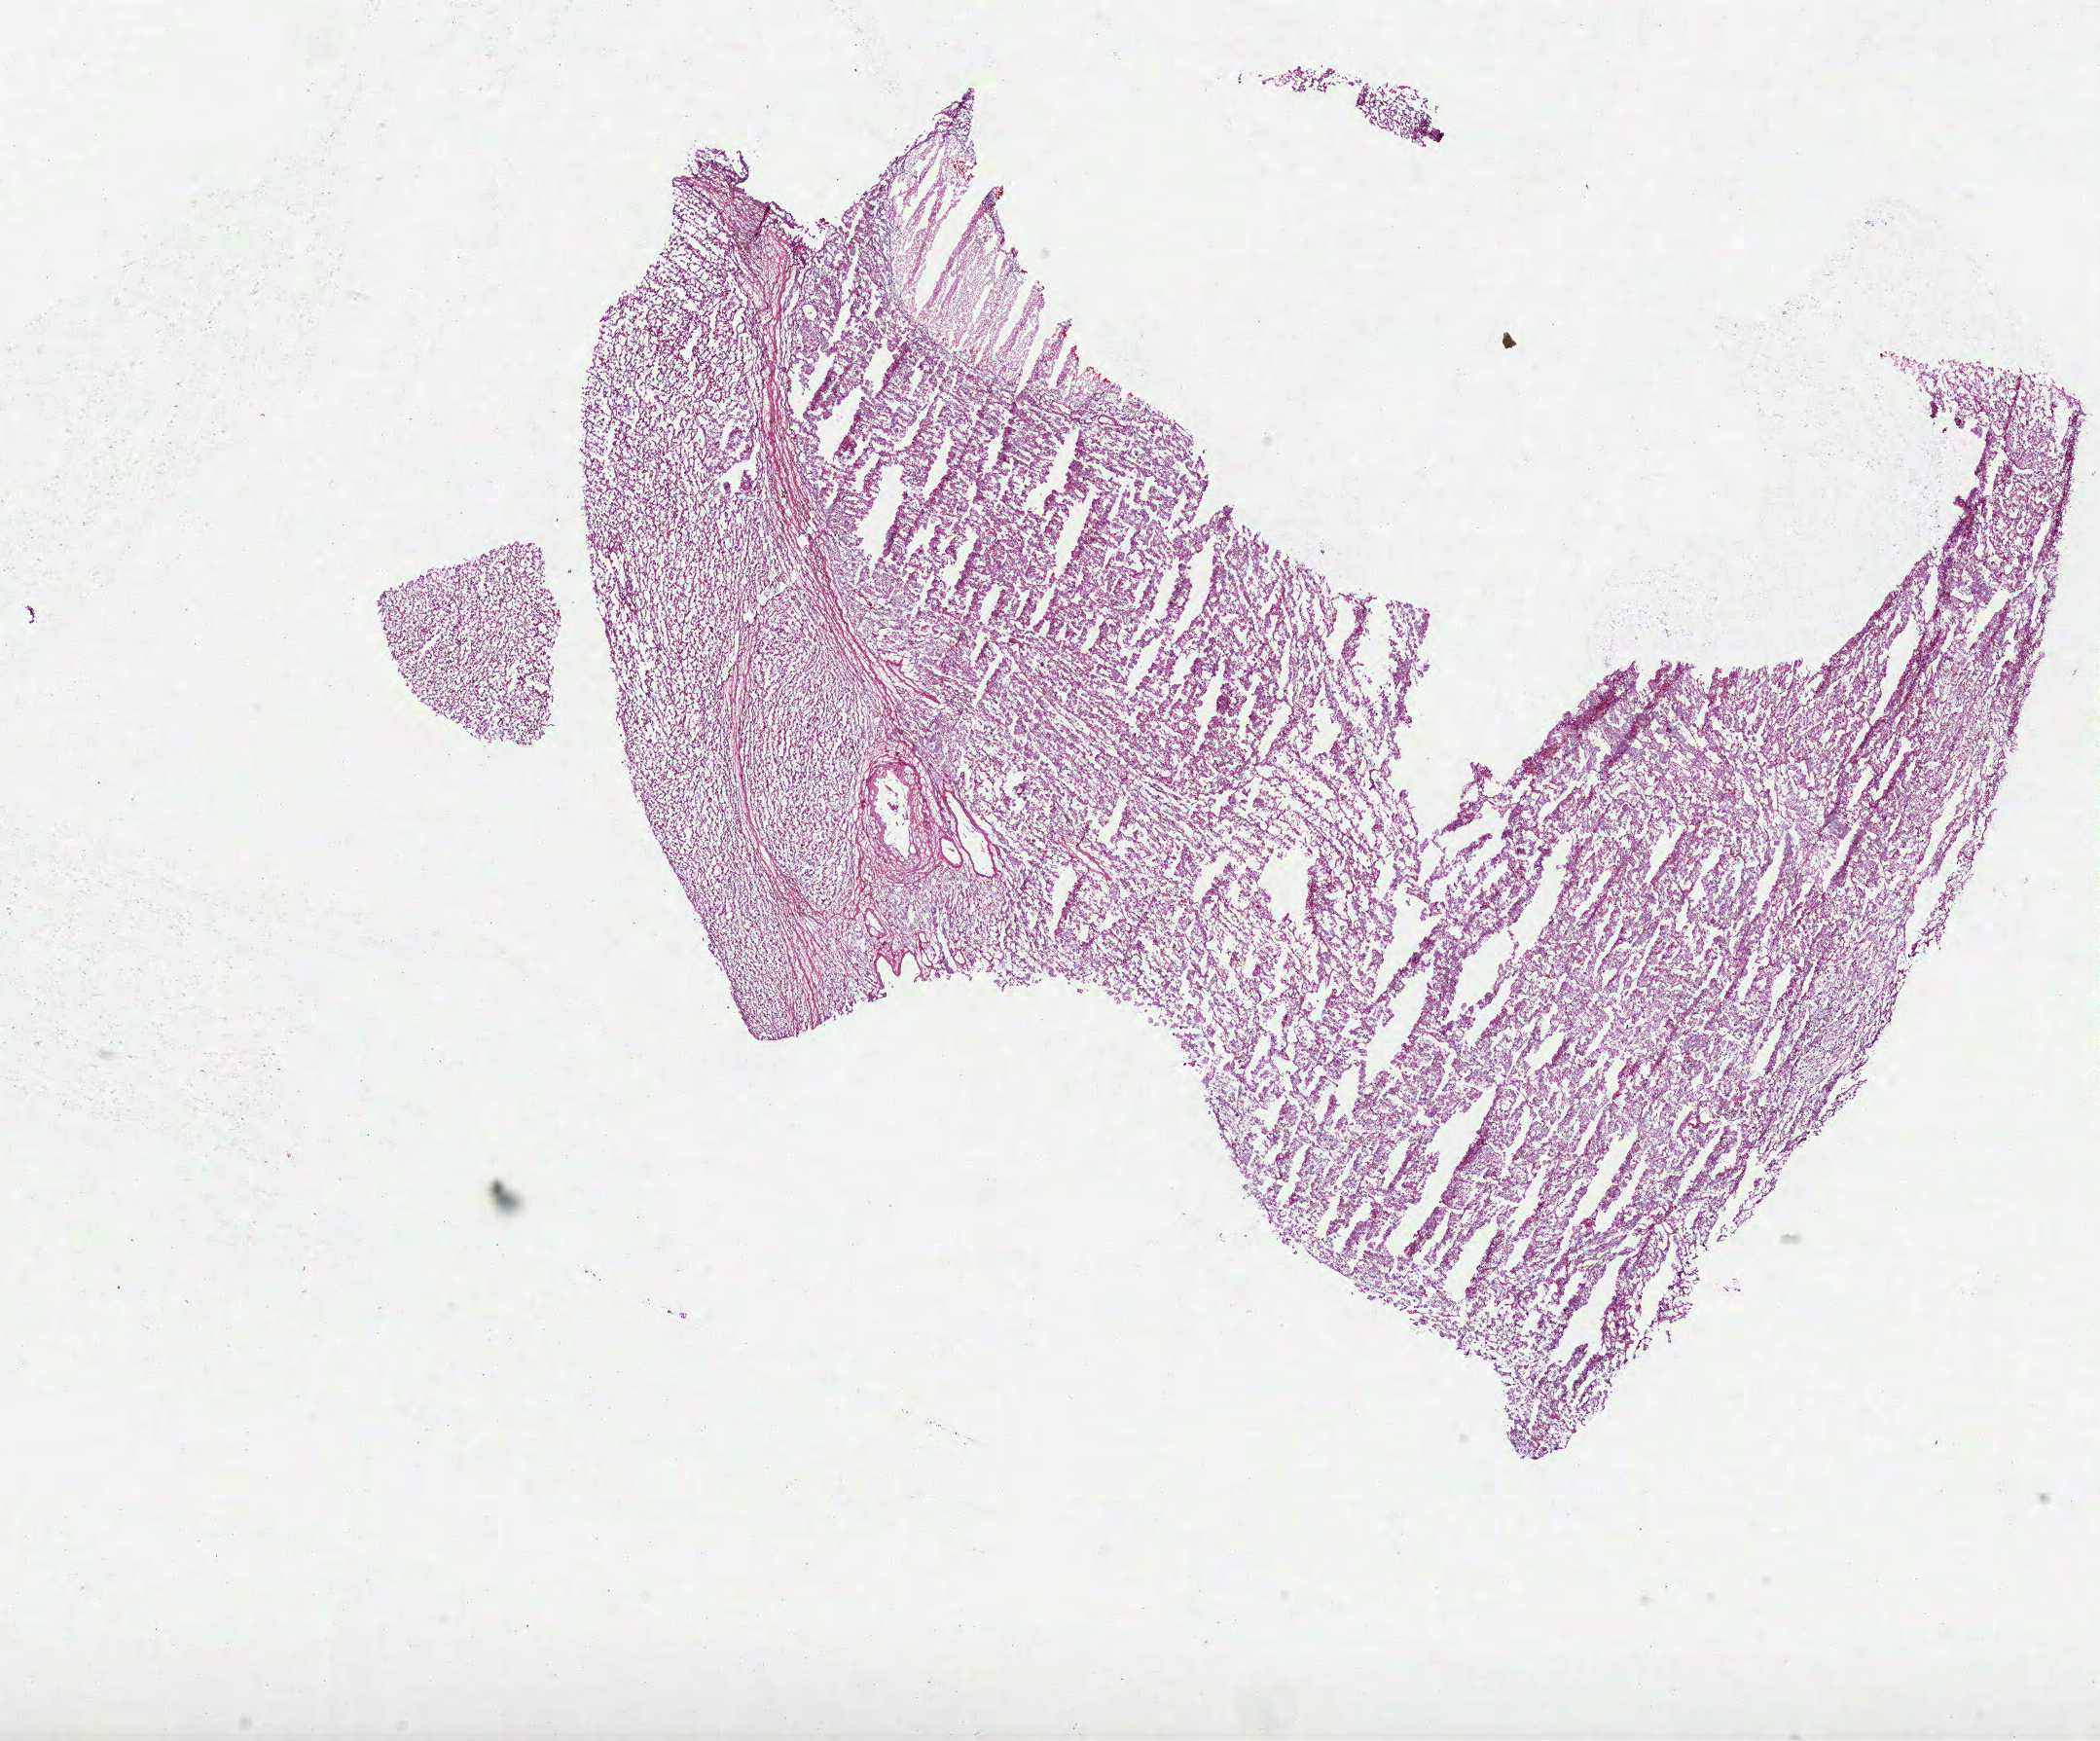
Hematoxylin and eosin (H&E) stained whole-slide image — whole scanned area (about 17.4 x 14.4 mm) shown as a low-resolution overview. Frozen section from the bottom of the tissue portion. Primary tumour sample from the kidney. Patient: female, age at initial diagnosis 46 years. Slide review estimates, as recorded: tumour cells 100%, tumour nuclei 90%, normal cells 0%, stromal cells 0%, necrosis 0%. Inflammatory infiltration, as recorded: lymphocyte infiltration 0%, monocyte infiltration 0%, neutrophil infiltration 0%.
Laterality: left. AJCC pathologic stage: III (6th edition). Histologic diagnosis: Renal cell carcinoma, chromophobe type.